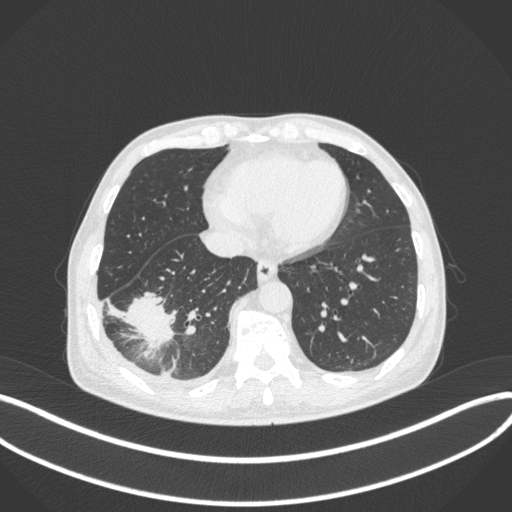
Chest CT, one axial slice; position 114 of 385 along the scan axis; 120 kVp; lung window (W 1500 / L -600 HU); 512 × 512 image matrix, field of view 400 × 400 mm. Male patient, age 64 years. Case-level facts recorded for this patient, not image findings: clinical TNM (as recorded): T3 N0 M0.
Outlined on this slice (bounding box drawn by a radiologist):
- lung tumour (recorded histology: adenocarcinoma): bounding box [x1, y1, x2, y2] px = [124, 288, 176, 358]